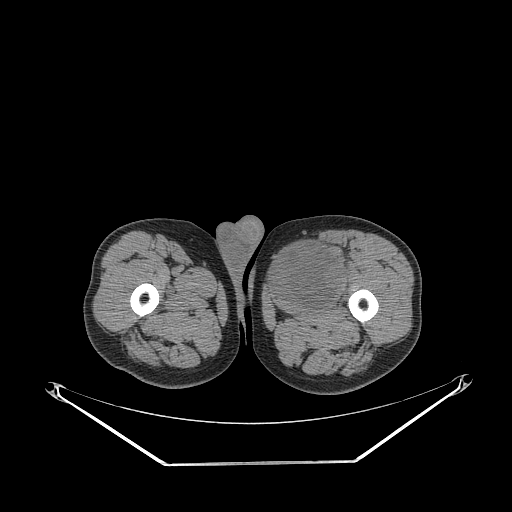
CT of an extremity soft-tissue mass (from a PET/CT study), one axial slice; position 257 of 267 along the scan axis; reconstruction kernel STANDARD; 140 kVp; soft-tissue window (W 400 / L 40 HU); 3.75 mm slice thickness; 512 × 512 image matrix, field of view 500 × 500 mm. Male patient. Case-level facts recorded for this patient, not image findings: histological type: pleiomorphic liposarcoma; grade: high; site of the primary tumour: left thigh.
Structures marked on this image (expert contour drawn on MRI and transferred to this co-registered scan by the dataset authors):
- gross tumour volume including surrounding oedema: bounding box <274,235,348,302> (left, top, right, bottom; pixels)
- gross tumour volume (mass): <274,244,344,302>